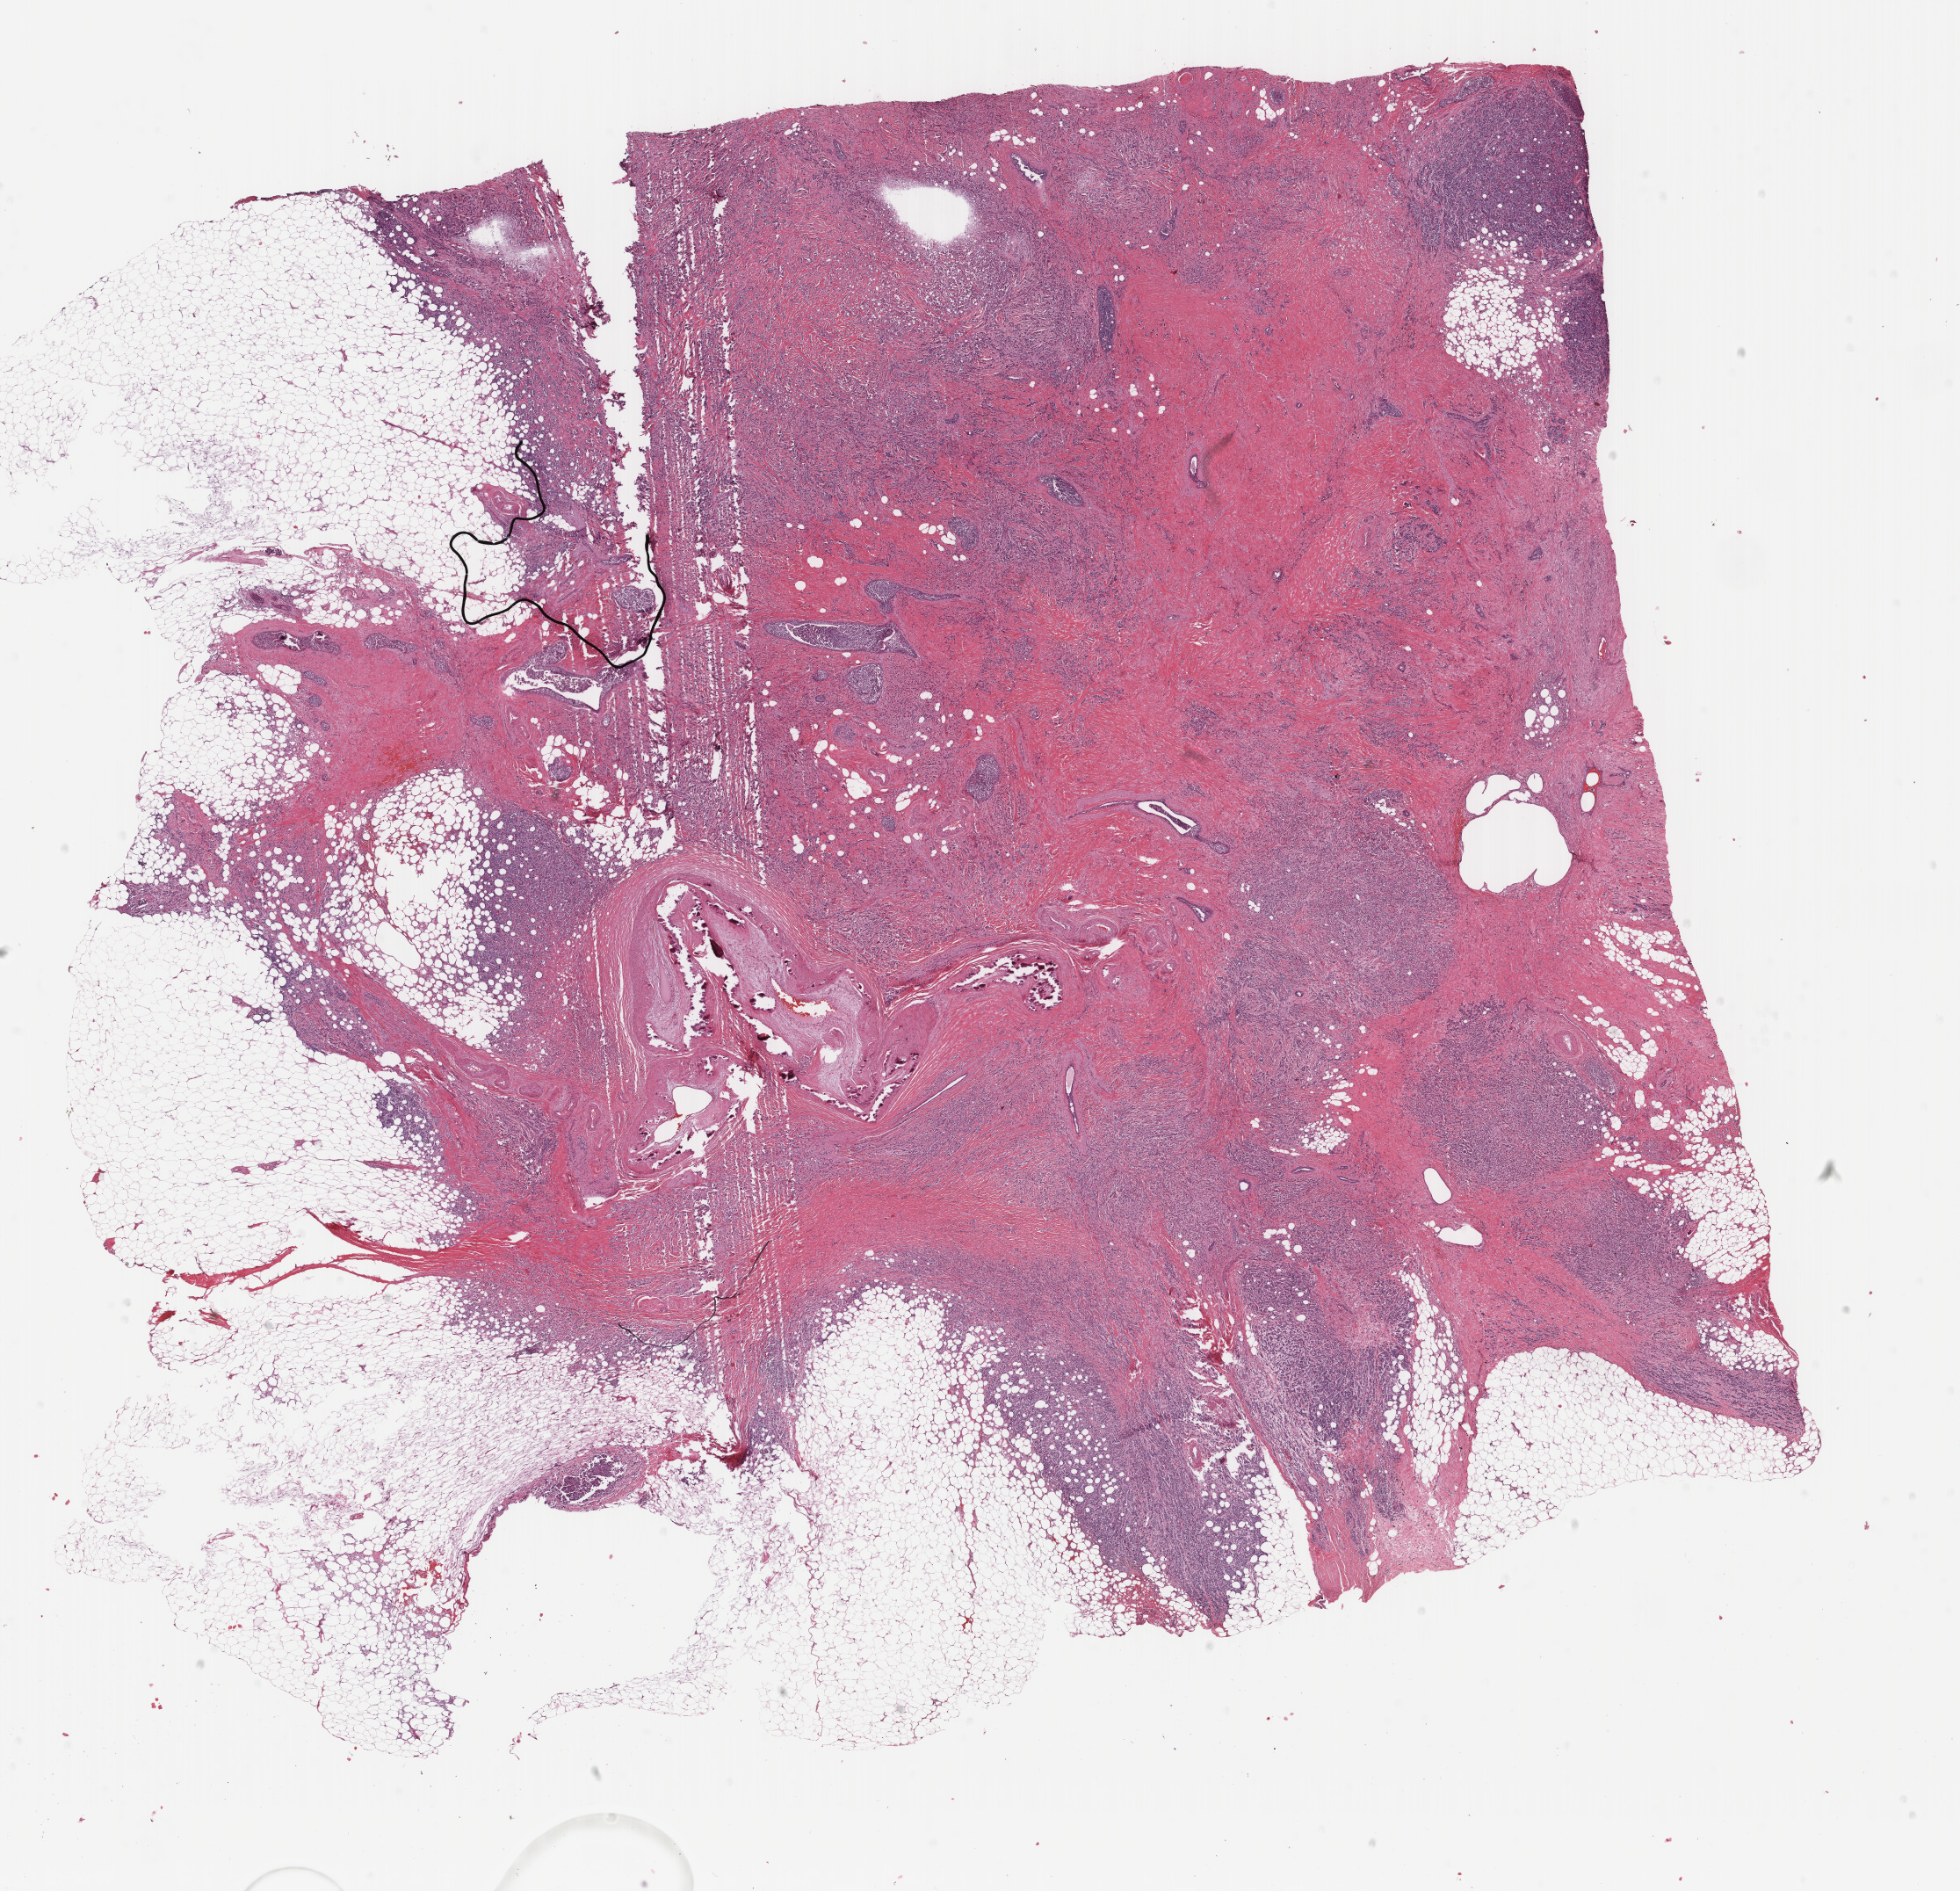
Whole-slide histology image, H&E-stained — low-resolution overview of the scanned area, about 17.7 x 17.1 mm. FFPE section. Primary tumour sample from the breast. Female, age 62 years at initial diagnosis.
Histologic diagnosis: Lobular carcinoma, NOS.